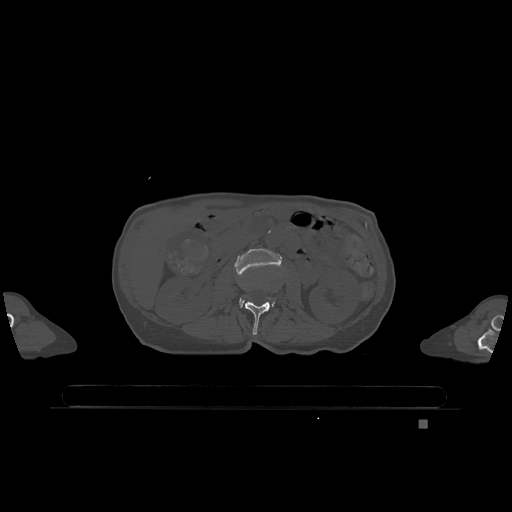
CT including the spine, one axial slice; slice 395 of 1317 in the series (ordered by position); bone window (W 1800 / L 400 HU); 0.5 mm slice thickness; 512 × 512 image matrix, field of view 500 × 500 mm. Female patient, age 74 years. From the clinical record (not read from this slice): primary cancer: lung; vertebrae with lytic lesions (as recorded): T1, T4, T5, T6, L4, L5.
Annotated regions visible in this slice (semi-automatic segmentation, software-assisted and operator-edited):
- L2 vertebra: bounding box <245,302,270,335> (left, top, right, bottom; pixels)
- L3 vertebra: <235,248,282,307>